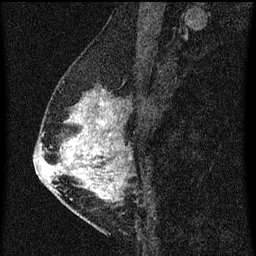
Breast MRI (dynamic contrast-enhanced), one sagittal slice. Slice 24 of 60 in the series (ordered by position). Dynamic contrast-enhanced series, image 2 of 3 at this slice position (ordered by acquisition). 1.5 T. TE 4.2 ms, TR 8 ms. 2 mm slice thickness. 256 × 256 image matrix, field of view 180 × 180 mm. Patient: female, 47 years.
Annotated regions visible in this slice (semi-automatically segmented with operator editing):
- analysis volume of interest (the breast-tissue region the enhancement analysis was run in; not a lesion): bounding box (x1, y1, x2, y2) in pixels: (50, 80, 139, 203)
- tumour enhancement mask (voxels above the 70 % enhancement threshold inside the analysis volume of interest): (57, 94, 128, 199)